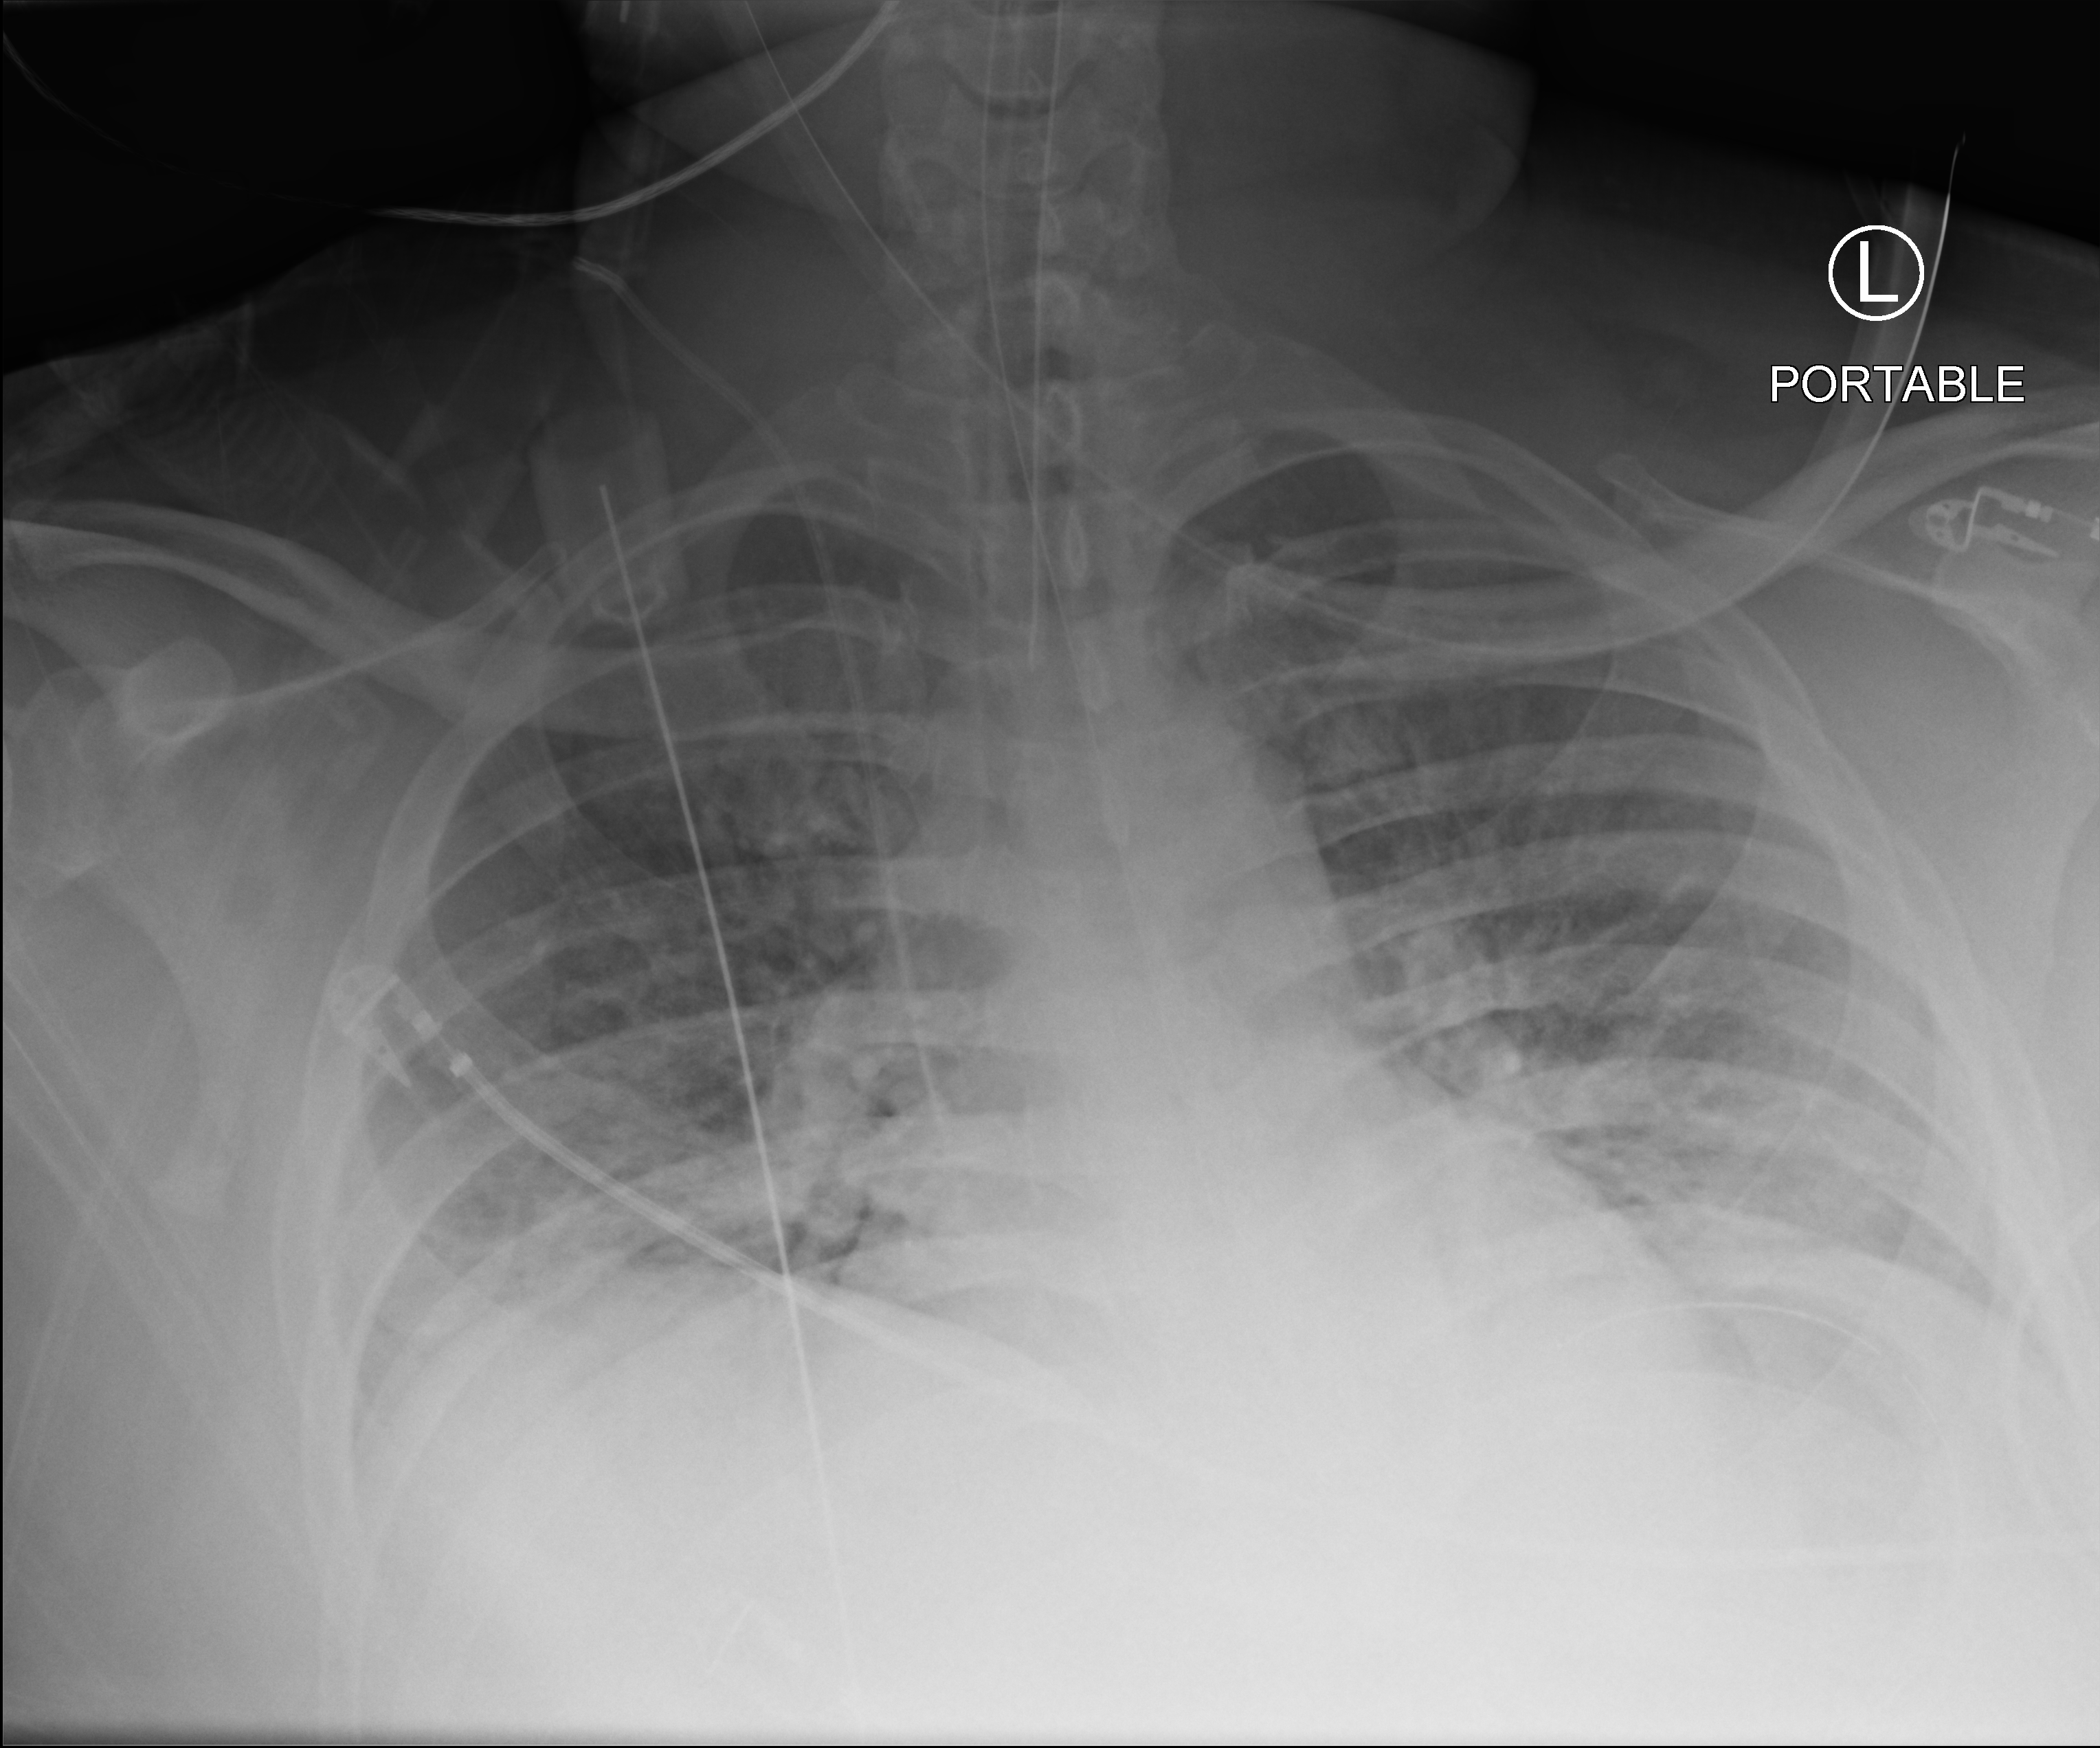
Chest X-ray (portable), anteroposterior (AP) projection. Male patient hospitalised with COVID-19, age 18–59 years.
Hospital-stay facts (about this admission, not read from this image; timing relative to this image not recorded): length of hospital stay: 69 days; mechanically ventilated during this hospital stay: yes.